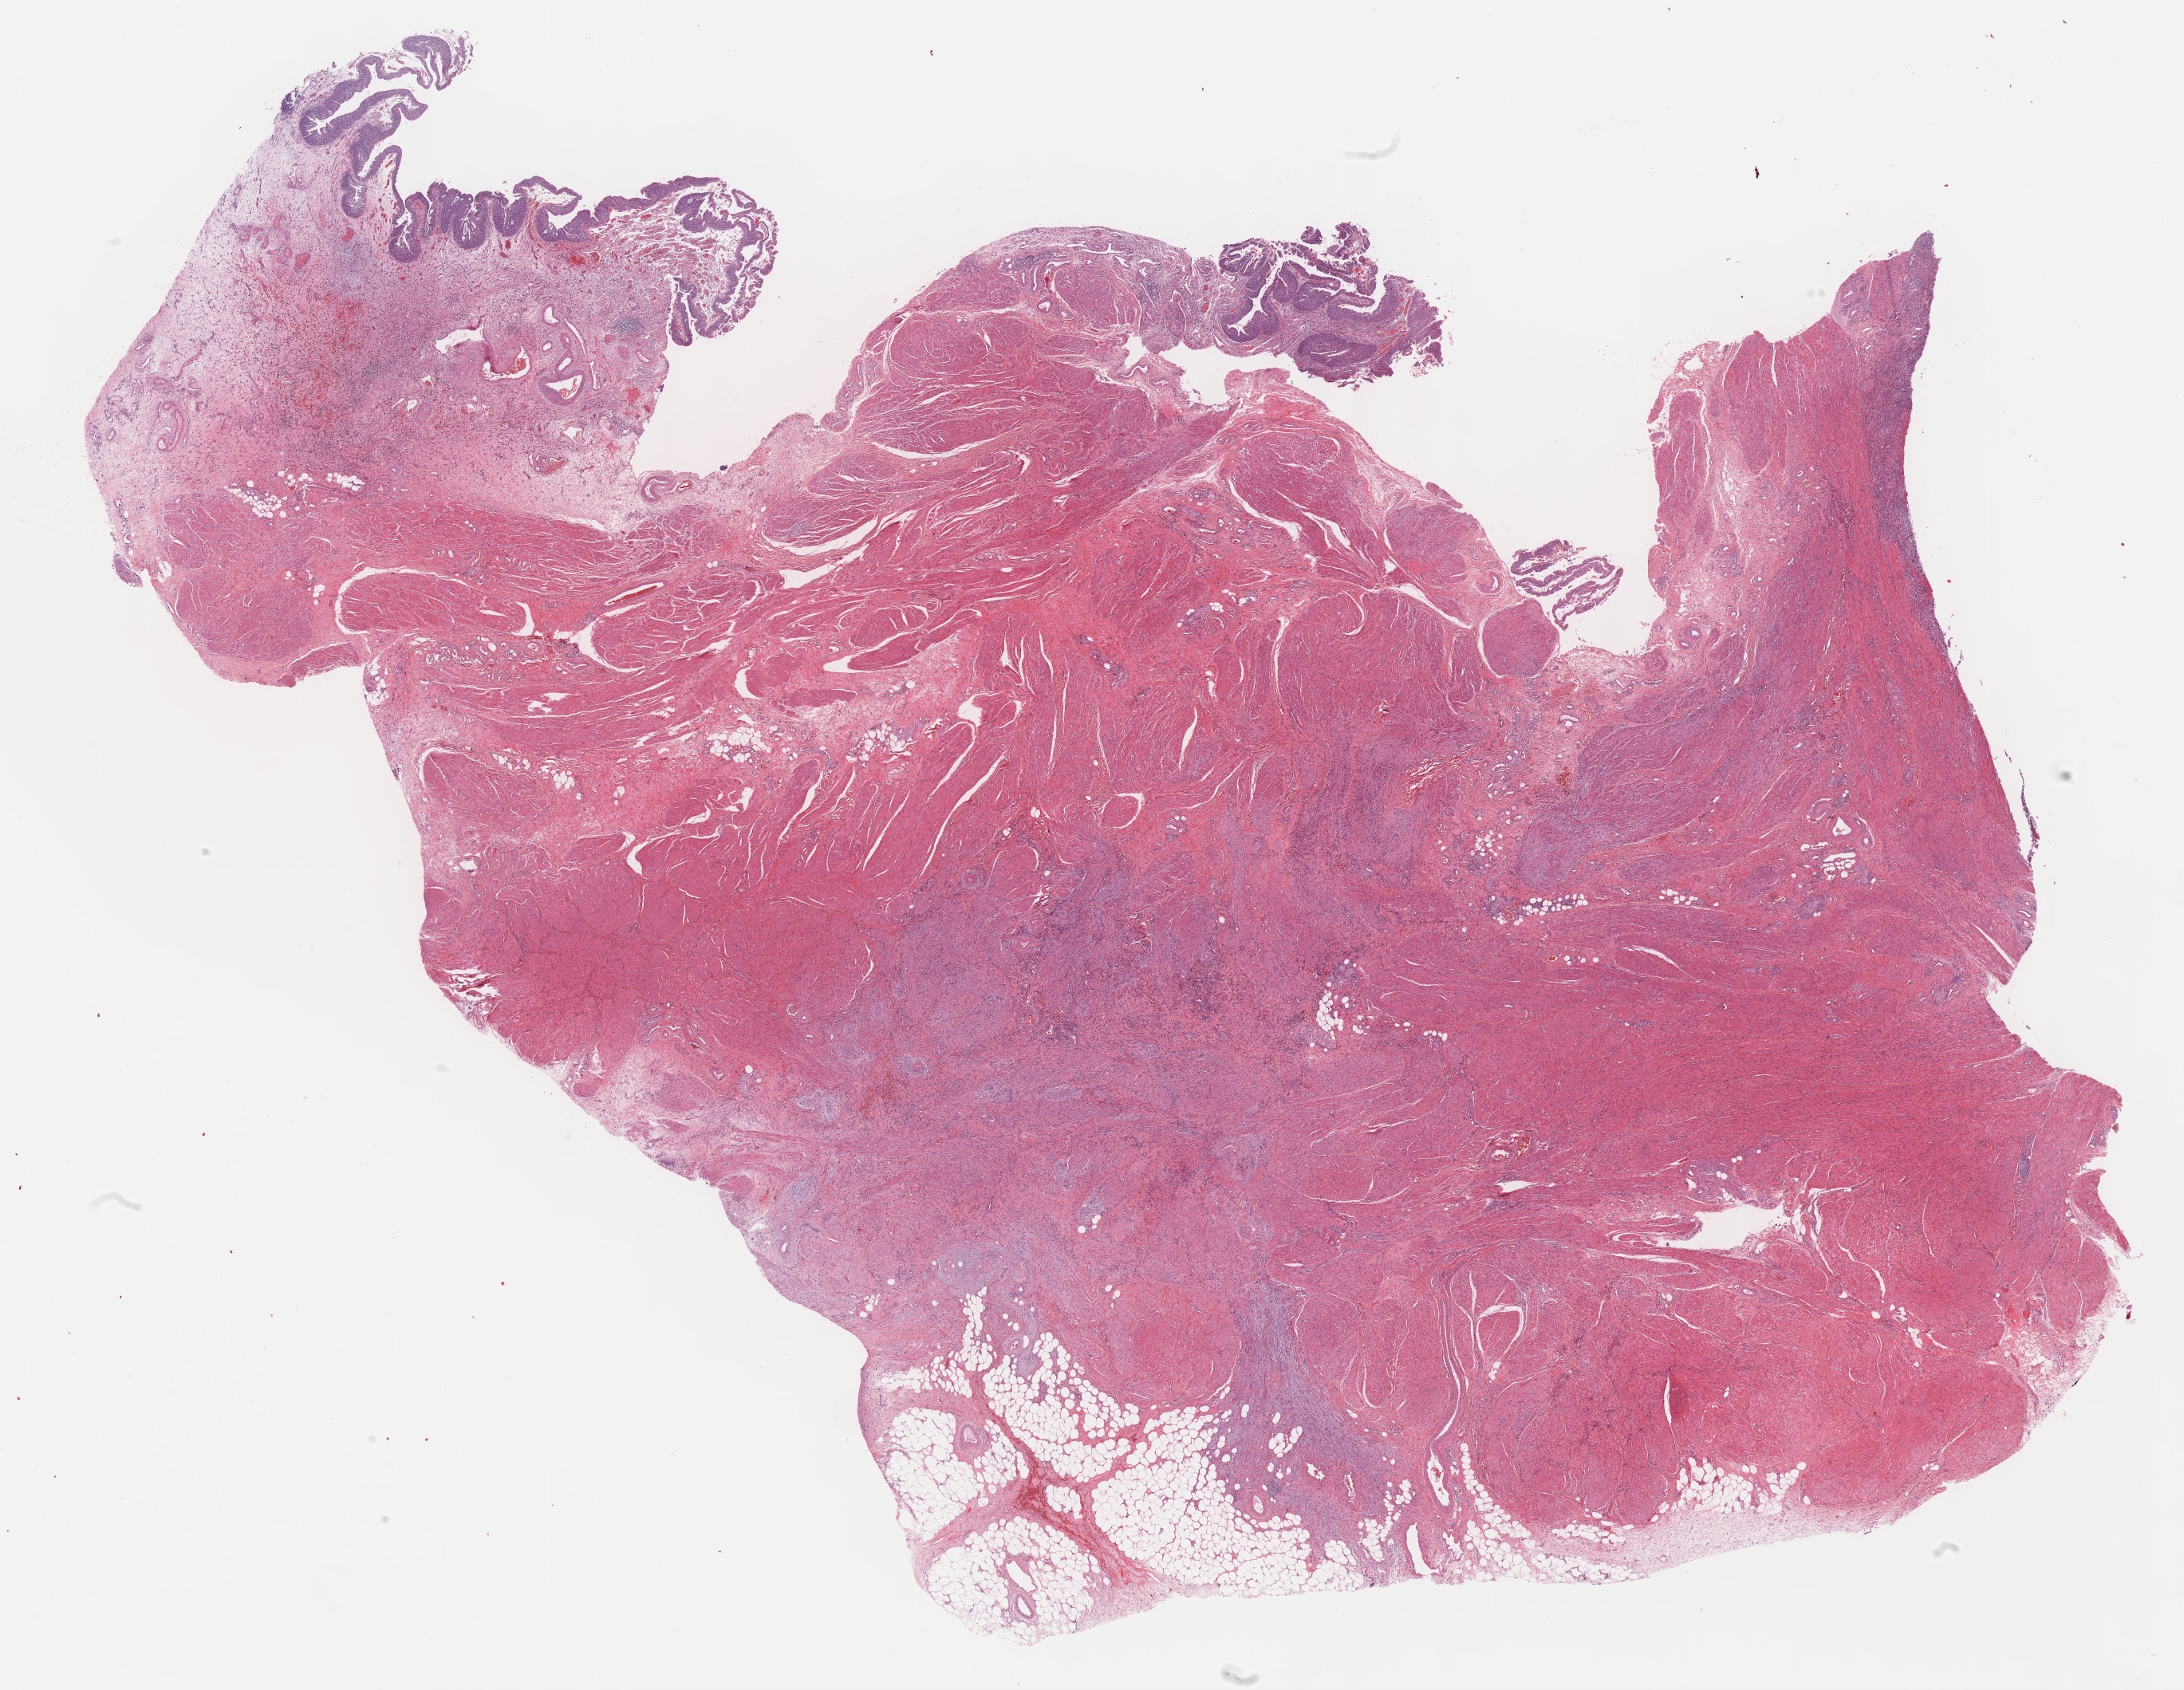
Digitized H&E-stained tissue section (whole slide), low-resolution overview of the scanned area, about 22.1 x 17.1 mm. Formalin-fixed paraffin-embedded (FFPE) diagnostic section. Primary tumour sample from the bladder. Male patient; age at initial diagnosis 70 years. Histologic grade: high grade.
Diagnosis: Transitional cell carcinoma. Lymph nodes positive (case pathology): 0 of 44 examined. AJCC pathologic stage: III (6th edition). TNM: T3b N0 M0.